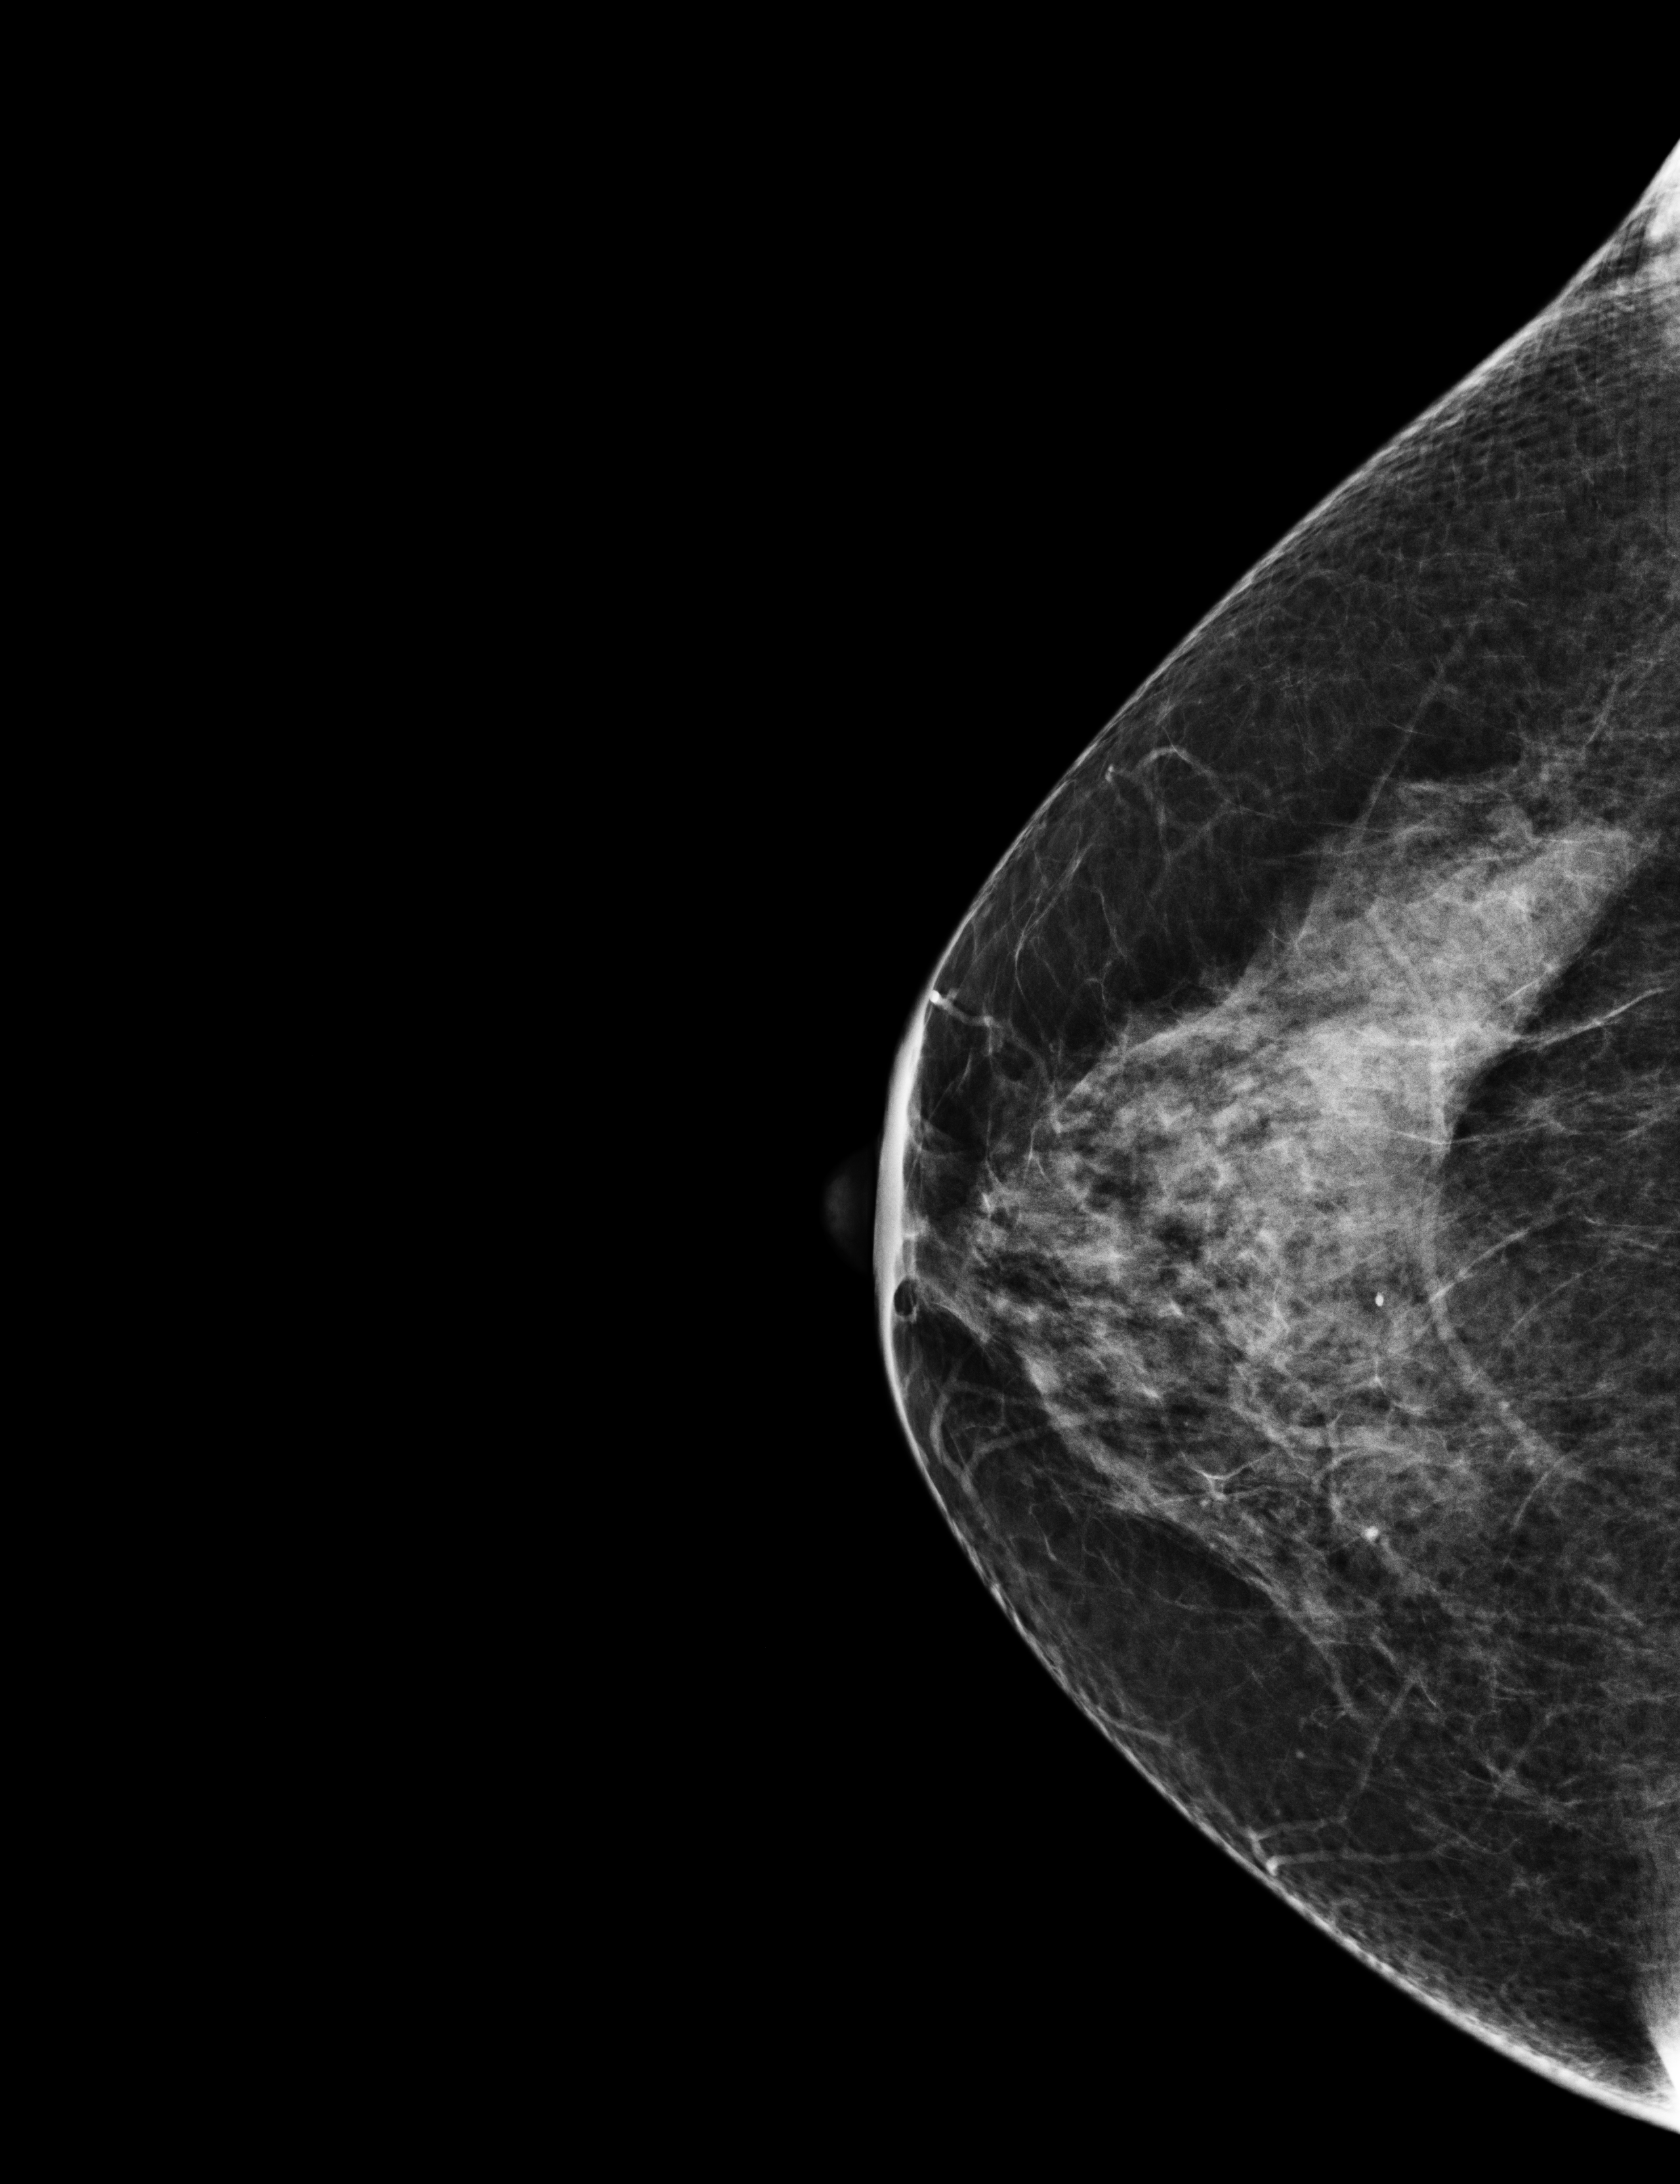
Annual screening mammography examination, compressed breast thickness 50 mm. Patient: female, 58 years.
Image type: full-field digital mammogram. Breast: right. Projection: CC view.